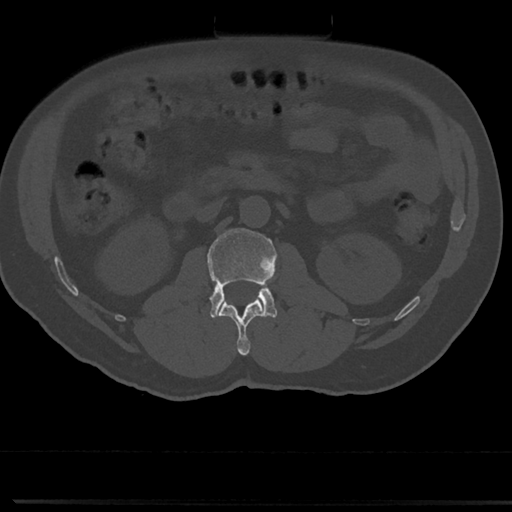
CT including the spine, one axial slice; reconstruction kernel Br40s/3; bone window (W 1800 / L 400 HU); 512 × 512 image matrix, field of view 355 × 355 mm. Patient: male, 61 years. From the clinical record (not read from this slice): primary cancer: prostate.
Outlined on this slice (semi-automatically segmented with operator editing):
- L1 vertebra: bounding box (x1, y1, x2, y2) in pixels: (219, 299, 264, 355)
- L2 vertebra: (207, 228, 276, 317)